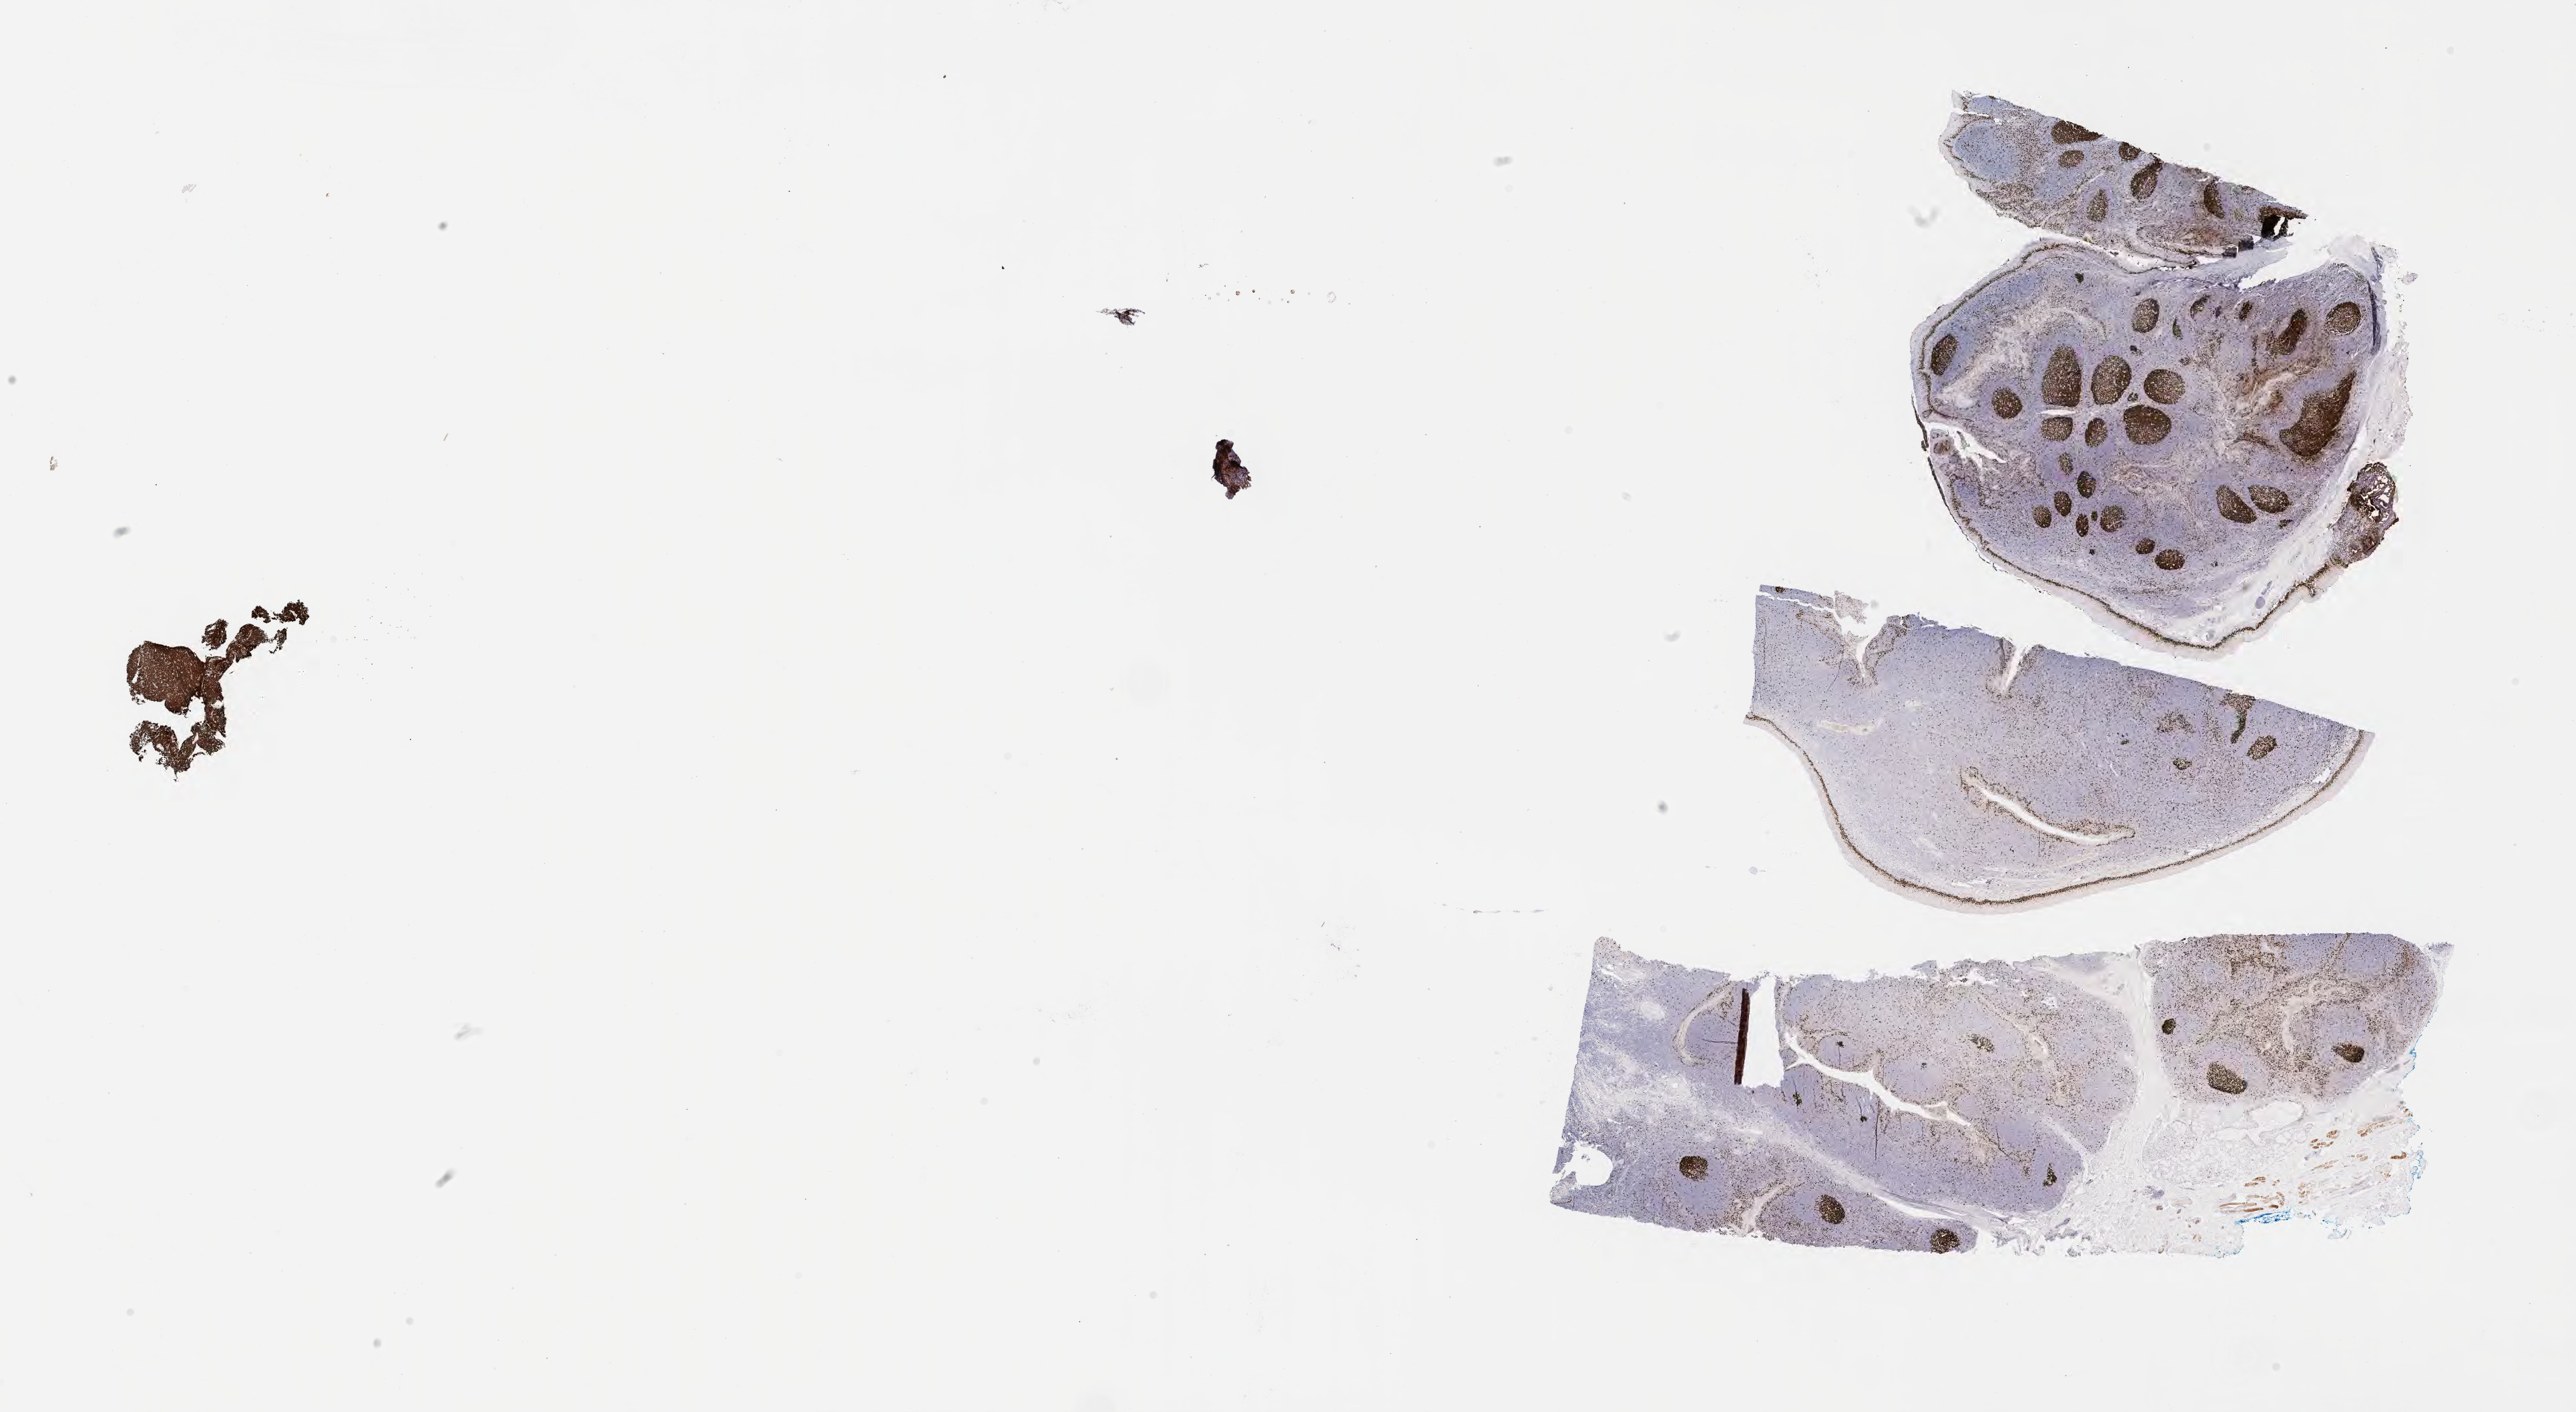
Immunohistochemistry (IHC) whole-slide image stained for Ki-67 — low-resolution overview of the scanned area, about 31.2 x 17.1 mm; specimen: tumor tissue. Patient: male, age at initial diagnosis 8 years.
Diagnosis: Burkitt lymphoma, NOS.